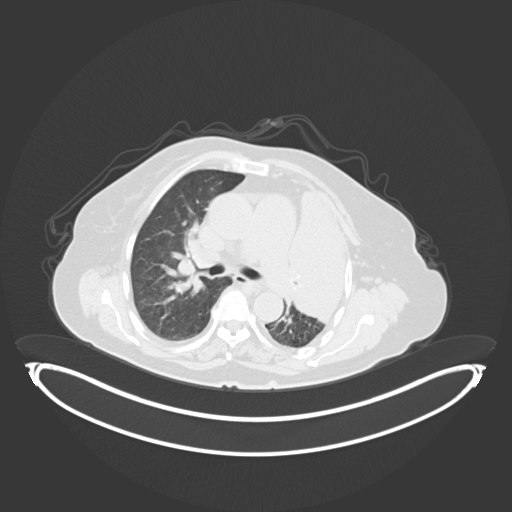
Chest CT, one axial slice. Position 207 of 284 along the scan axis. Reconstruction kernel B30f. 120 kVp. Lung window (W 1500 / L -600 HU). 3 mm slice thickness. 512 × 512 image matrix, field of view 500 × 500 mm. Female patient, age 75 years. Case-level facts recorded for this patient, not image findings: clinical TNM (as recorded): T3 N3 M1.
Outlined on this slice (rectangle marked by the reading radiologist):
- lung tumour (recorded histology: adenocarcinoma): bounding box (x1, y1, x2, y2) in pixels: (278, 180, 361, 327)